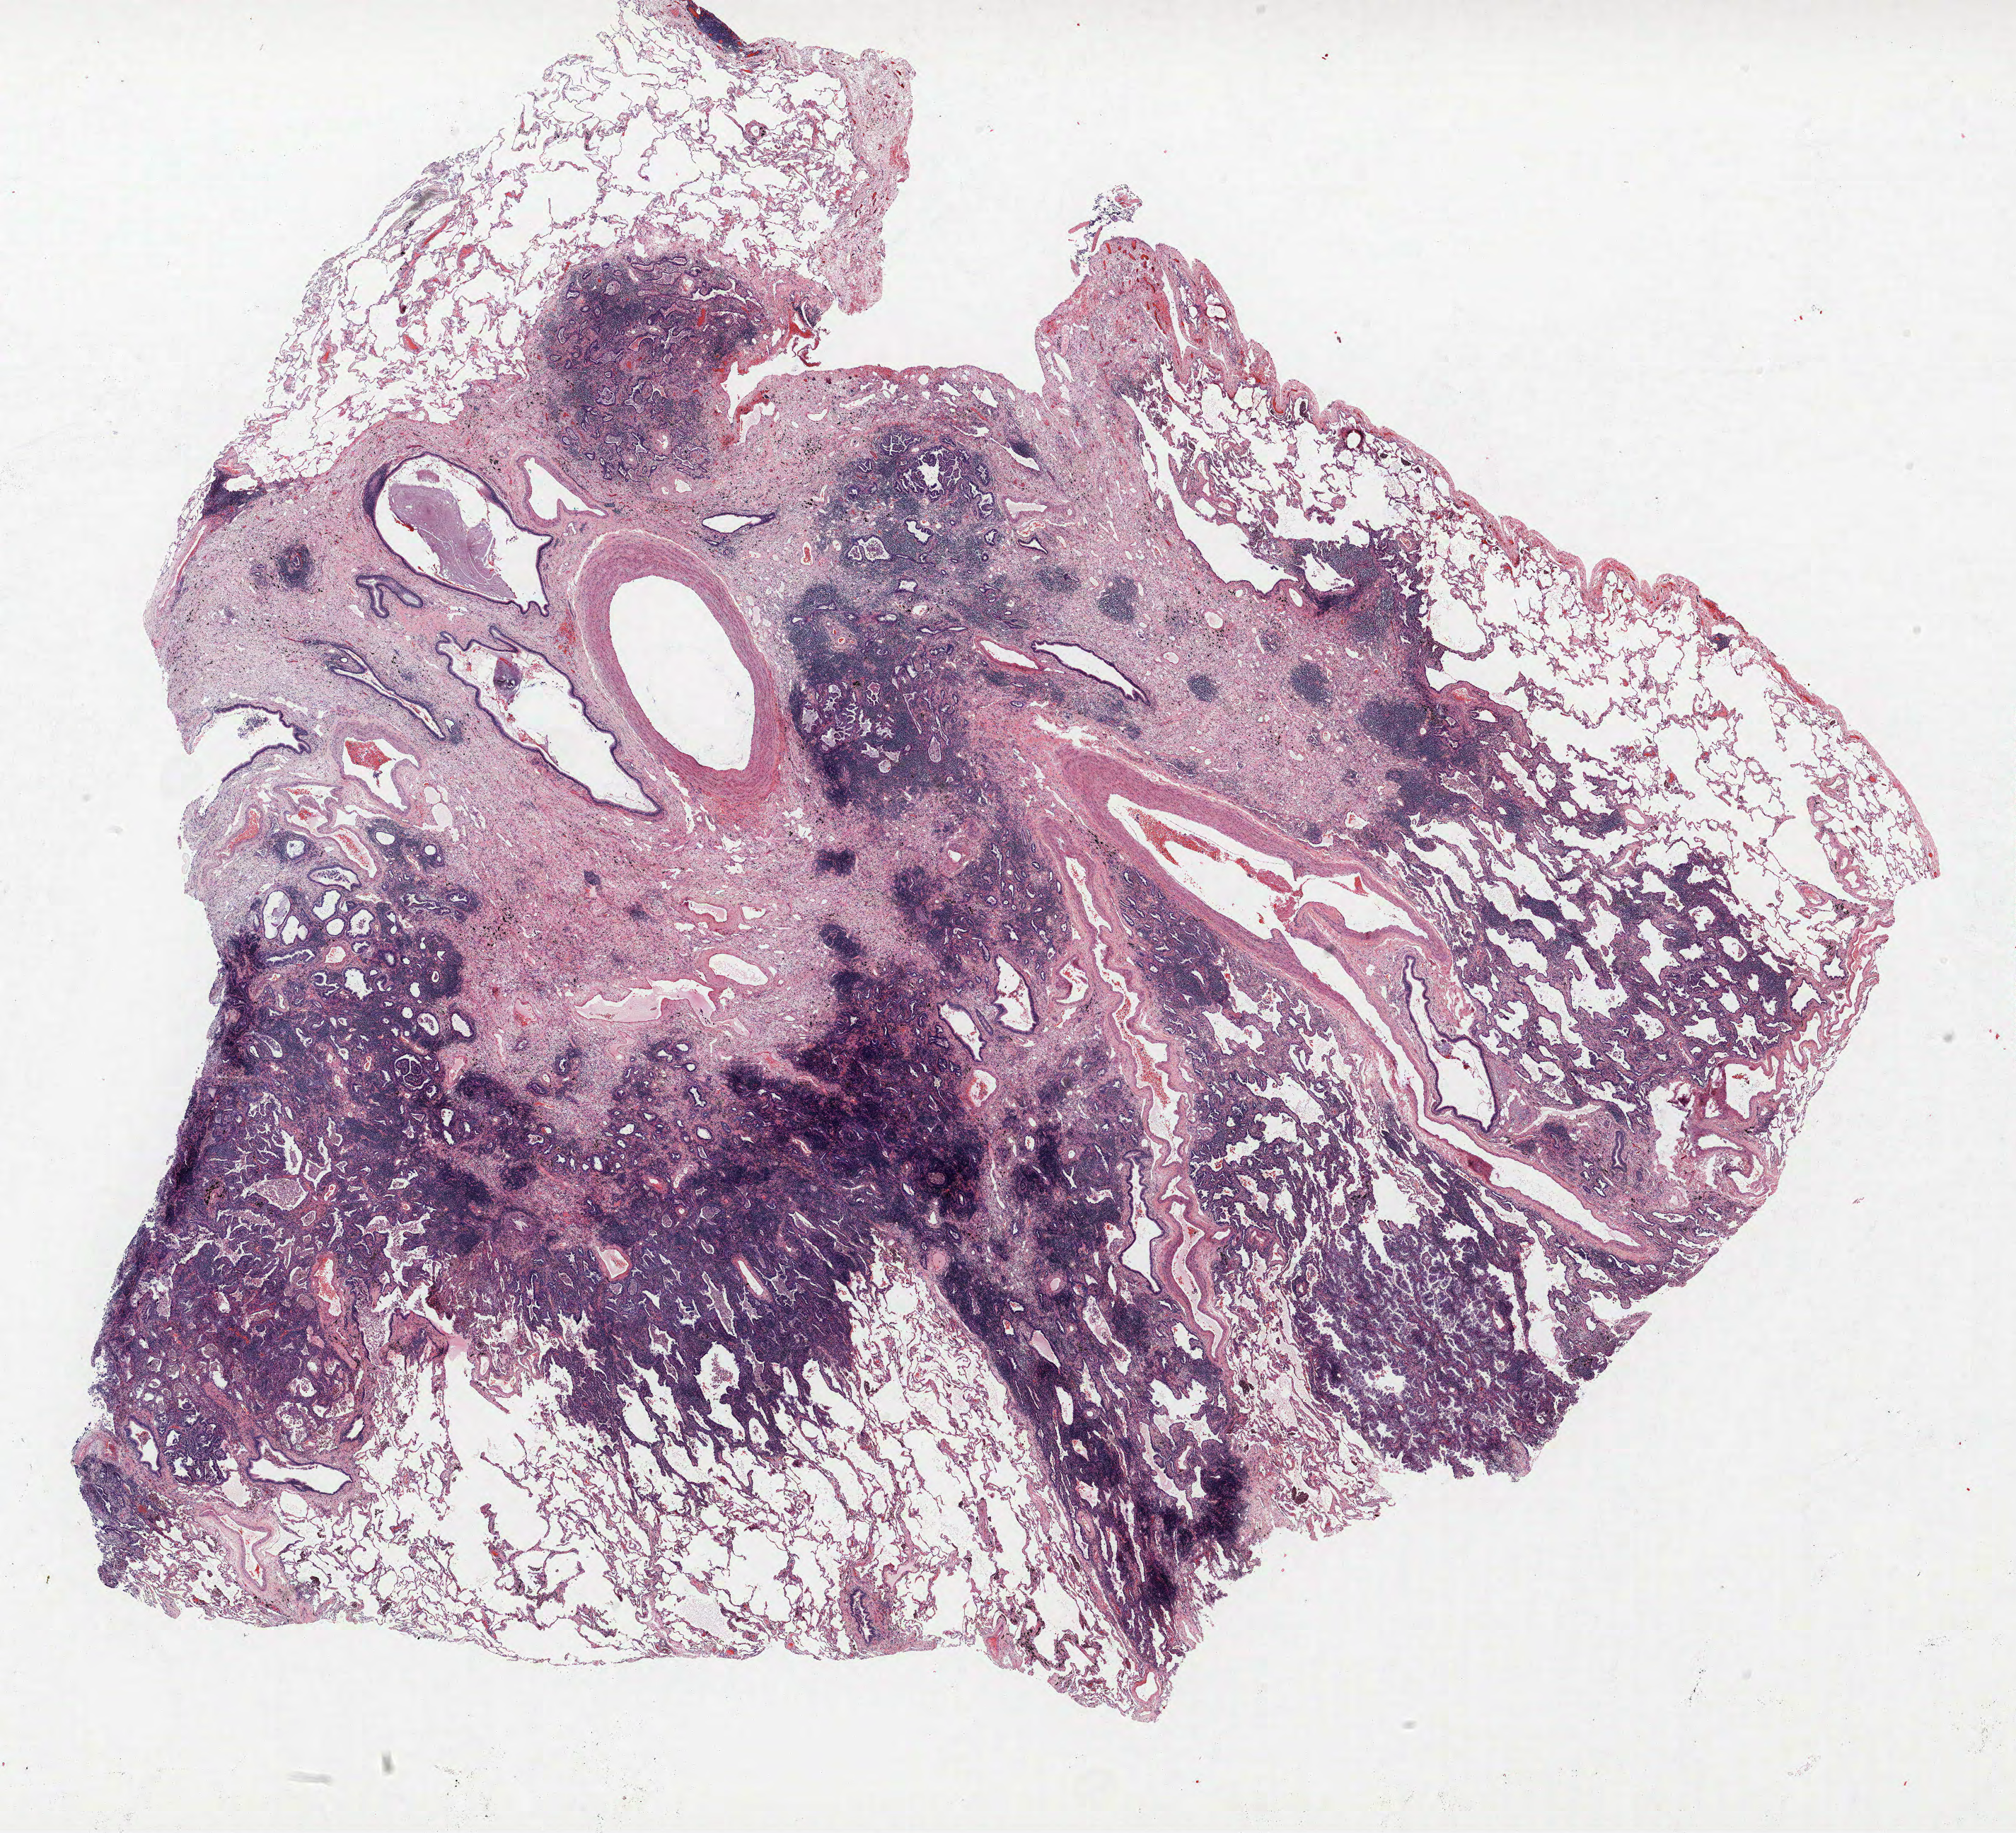
Whole-slide histology image, H&E, low-resolution overview of the scanned area, about 22.8 x 20.7 mm, formalin-fixed paraffin-embedded (FFPE) section, lung. Female, age 67 at enrolment. Current smoker at enrolment. Grade: well differentiated (G1).
* primary tumour location (clinical record): right middle lobe
* stage (AJCC 6th edition): IA
* tumour size (pathology): 25 mm
* participant's lung-cancer diagnosis: Bronchiolo-alveolar adenocarcinoma, NOS (ICD-O-3 8250/3)